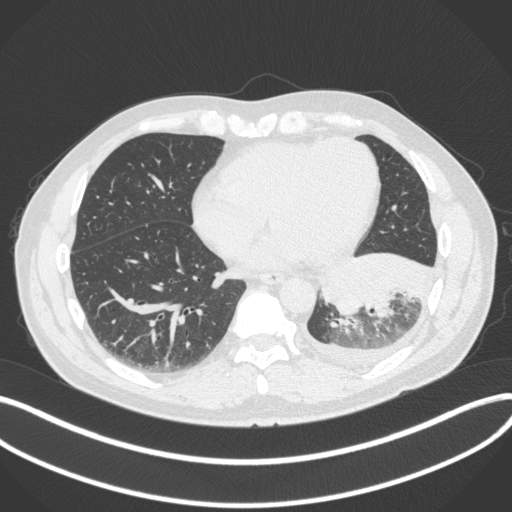
Chest CT, one axial slice. Position 122 of 350 along the scan axis. Reconstruction kernel B31f. 120 kVp. Lung window (W 1500 / L -600 HU). 512 × 512 image matrix, field of view 400 × 400 mm. Male patient, age 58 years. Case-level facts recorded for this patient, not image findings: clinical TNM (as recorded): T3 N1 M1b; histopathological grade: G3.
Outlined on this slice (rectangle marked by the reading radiologist):
- lung tumour (recorded histology: small cell carcinoma): box from (x=317, y=248) to (x=438, y=317) px